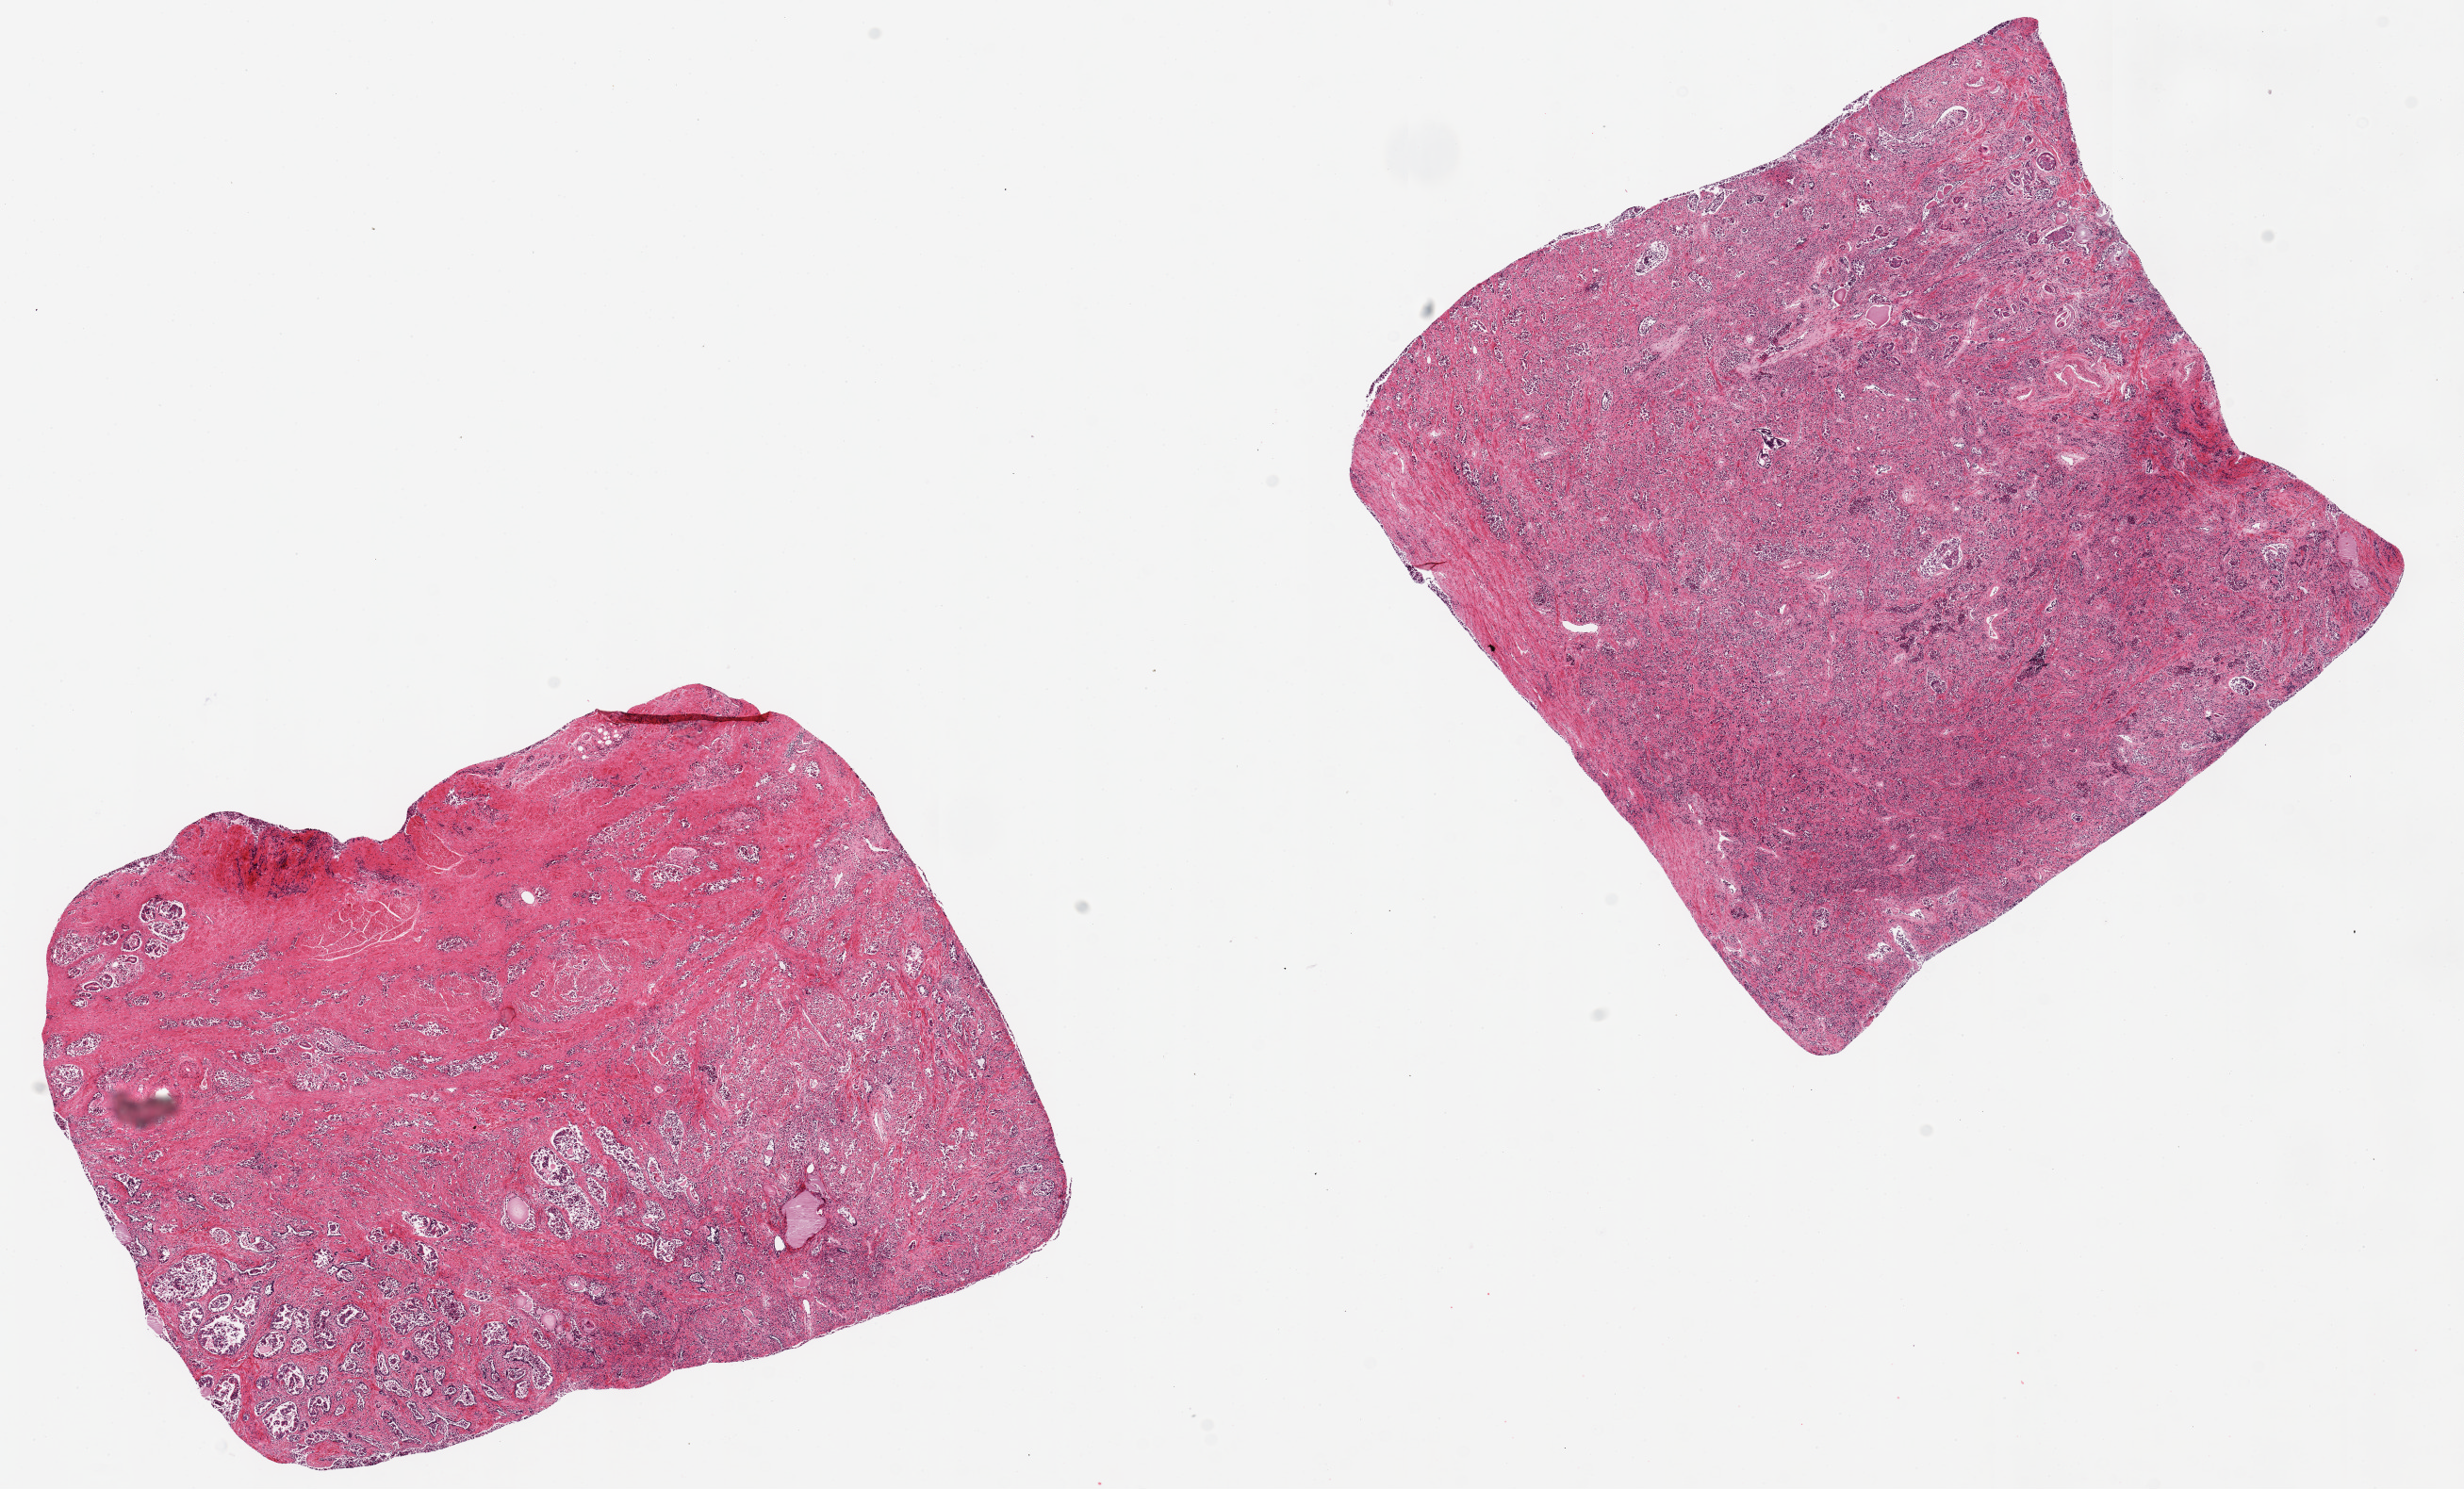
Whole-slide image, hematoxylin and eosin (H&E) stain — shown as a low-resolution overview of the whole scanned area (about 20.7 x 12.5 mm). PAXgene-fixed paraffin-embedded (PFPE) section. Sampled site (target tissue): prostate. Tissue donor sample. Male donor.
Review note (as recorded): 2 pieces, 7x6 & 7x7mm; glands autolyzed.